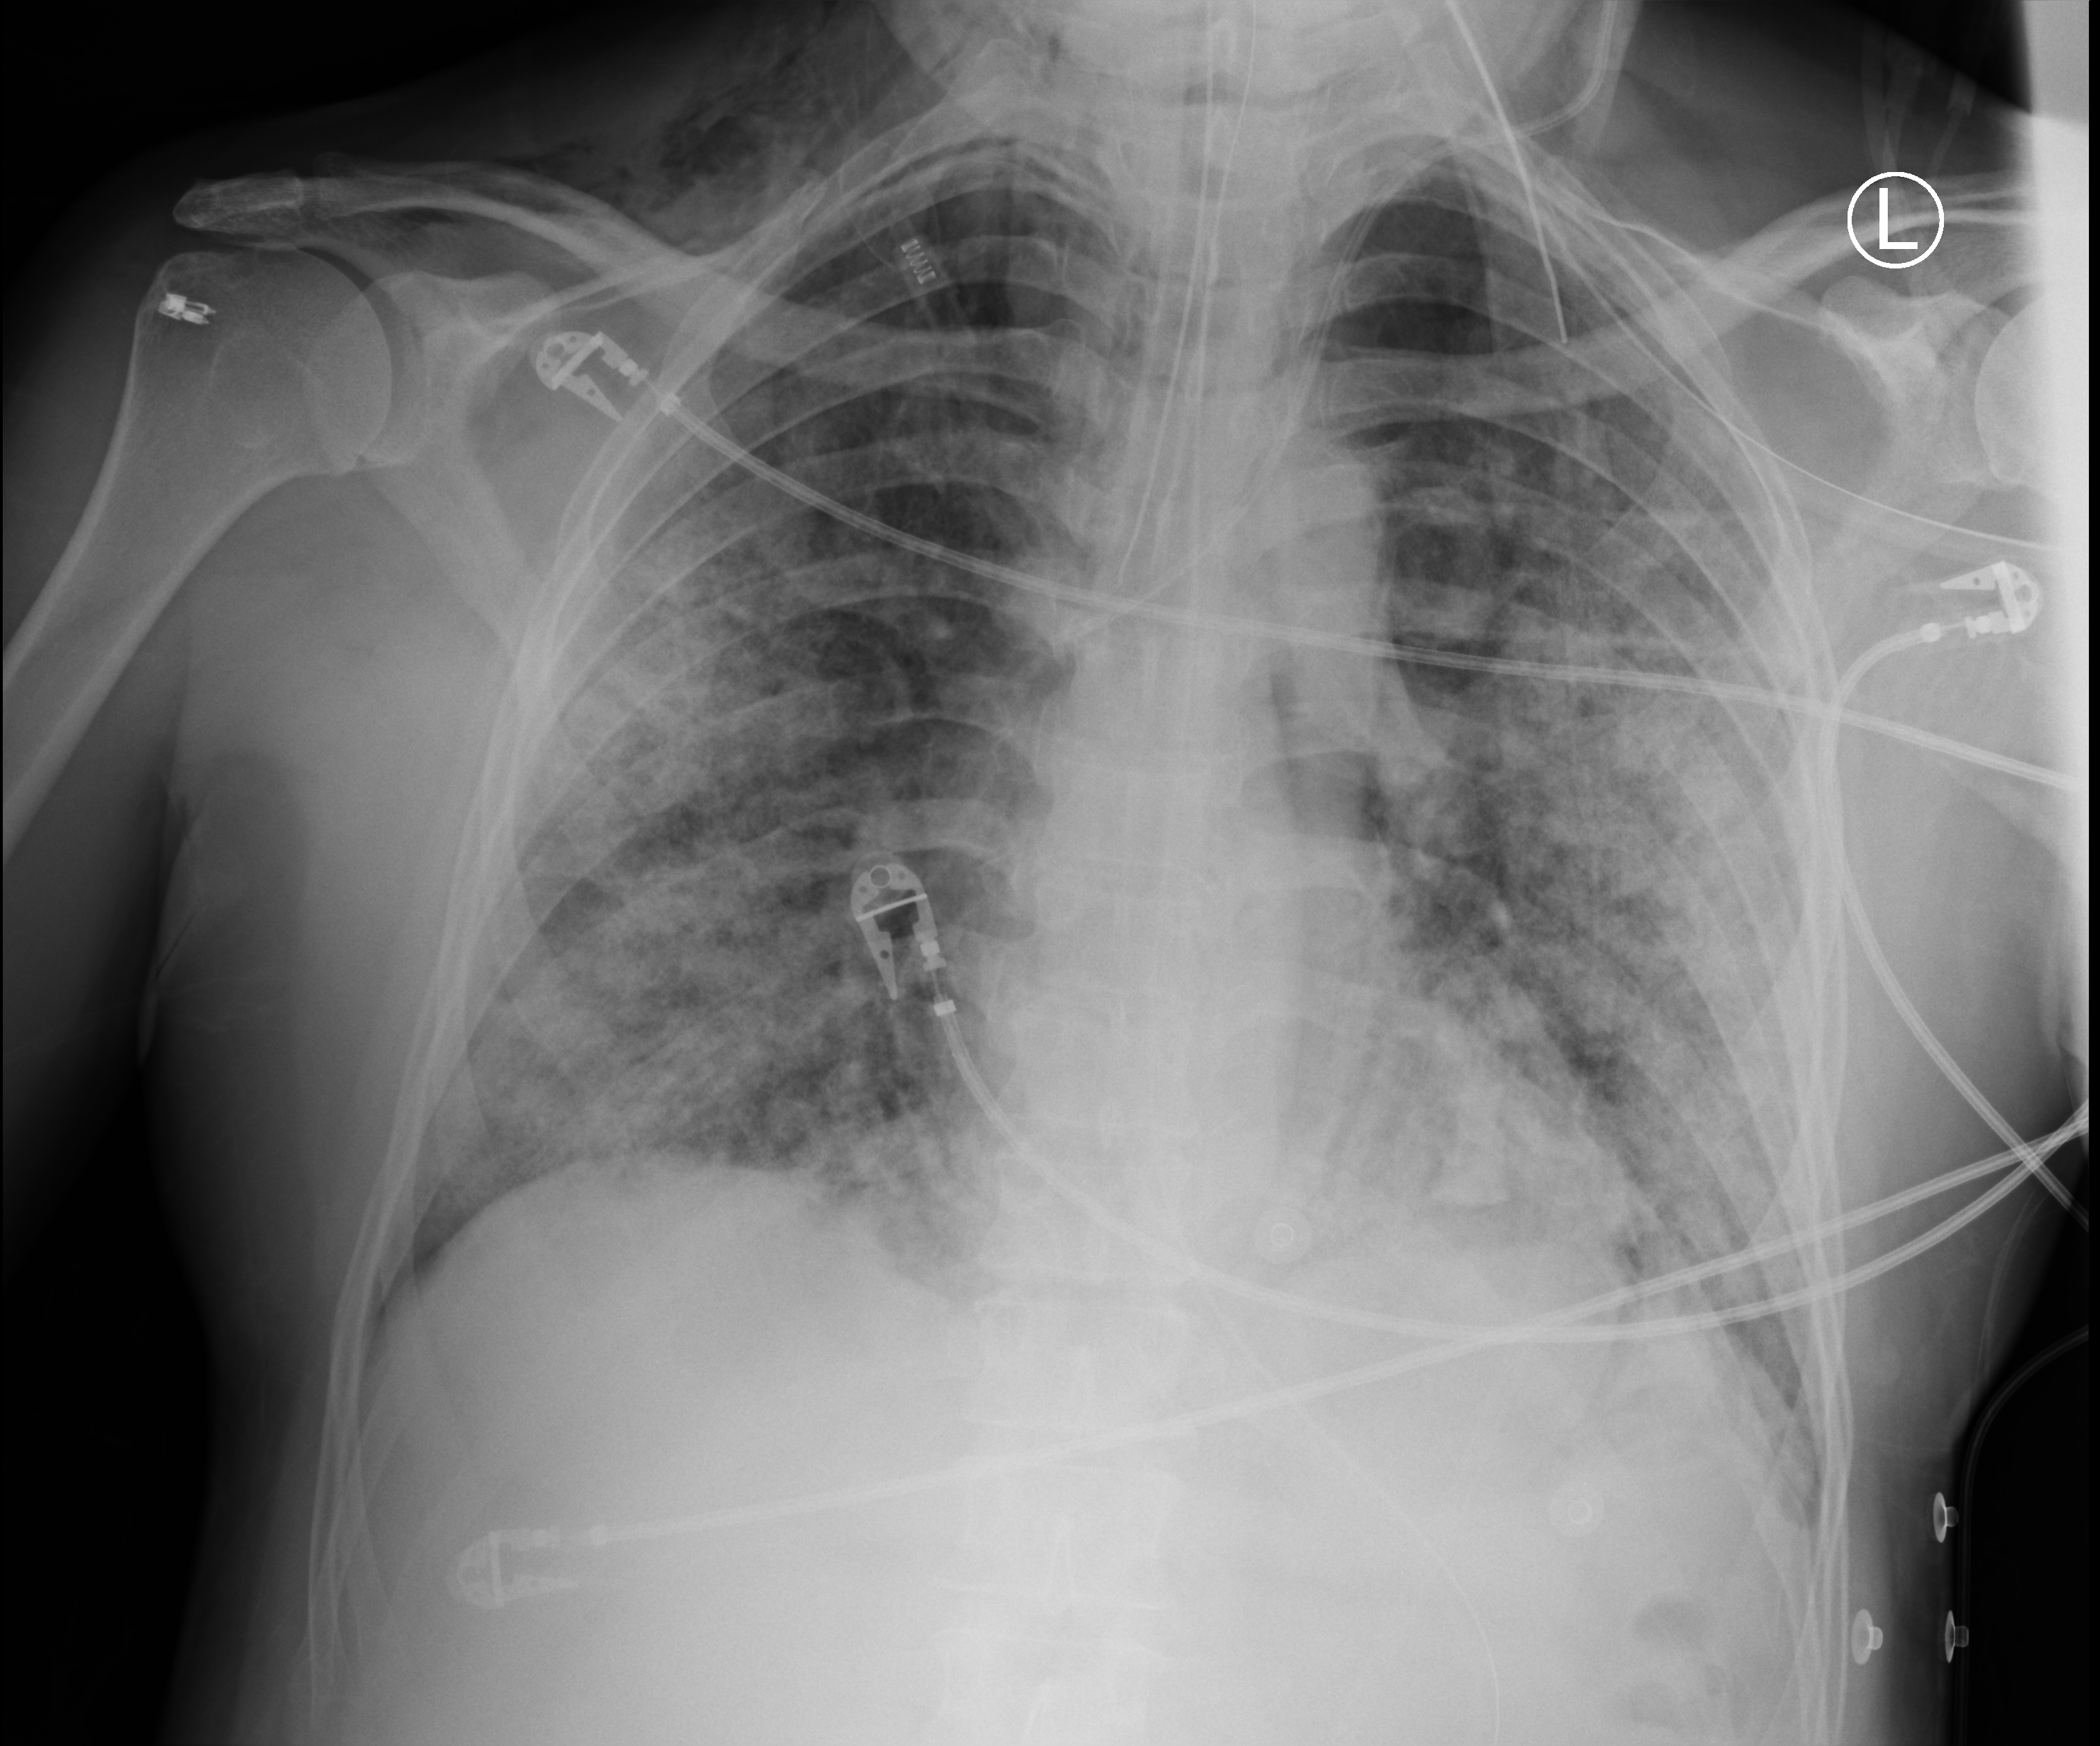
Portable chest radiograph, anteroposterior (AP) projection. Patient hospitalised with COVID-19; male, aged 60–74 years.
Hospital-stay facts (about this admission, not read from this image; timing relative to this image not recorded): admitted to intensive care during this hospital stay: yes; mechanically ventilated during this hospital stay: yes.